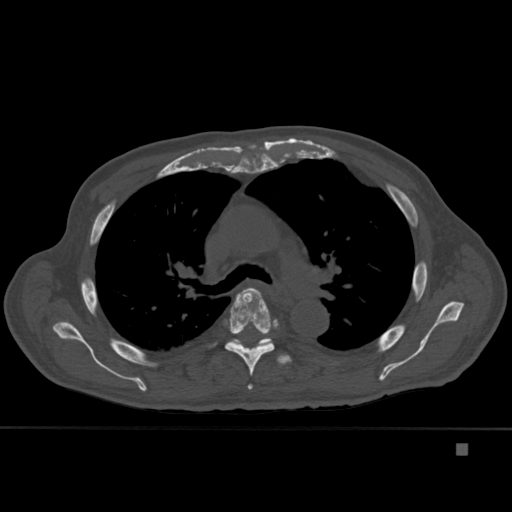
CT including the spine, one axial slice; bone window (W 1800 / L 400 HU); 512 × 512 image matrix, field of view 378 × 378 mm. Male patient, age 75 years. Case-level facts recorded for this patient, not image findings: primary cancer: prostate.
Structures marked on this image (semi-automatically segmented with operator editing):
- T4 vertebra: bounding box <247,384,253,390> (left, top, right, bottom; pixels)
- T5 vertebra: <225,287,279,376>
- T6 vertebra: <233,338,292,365>